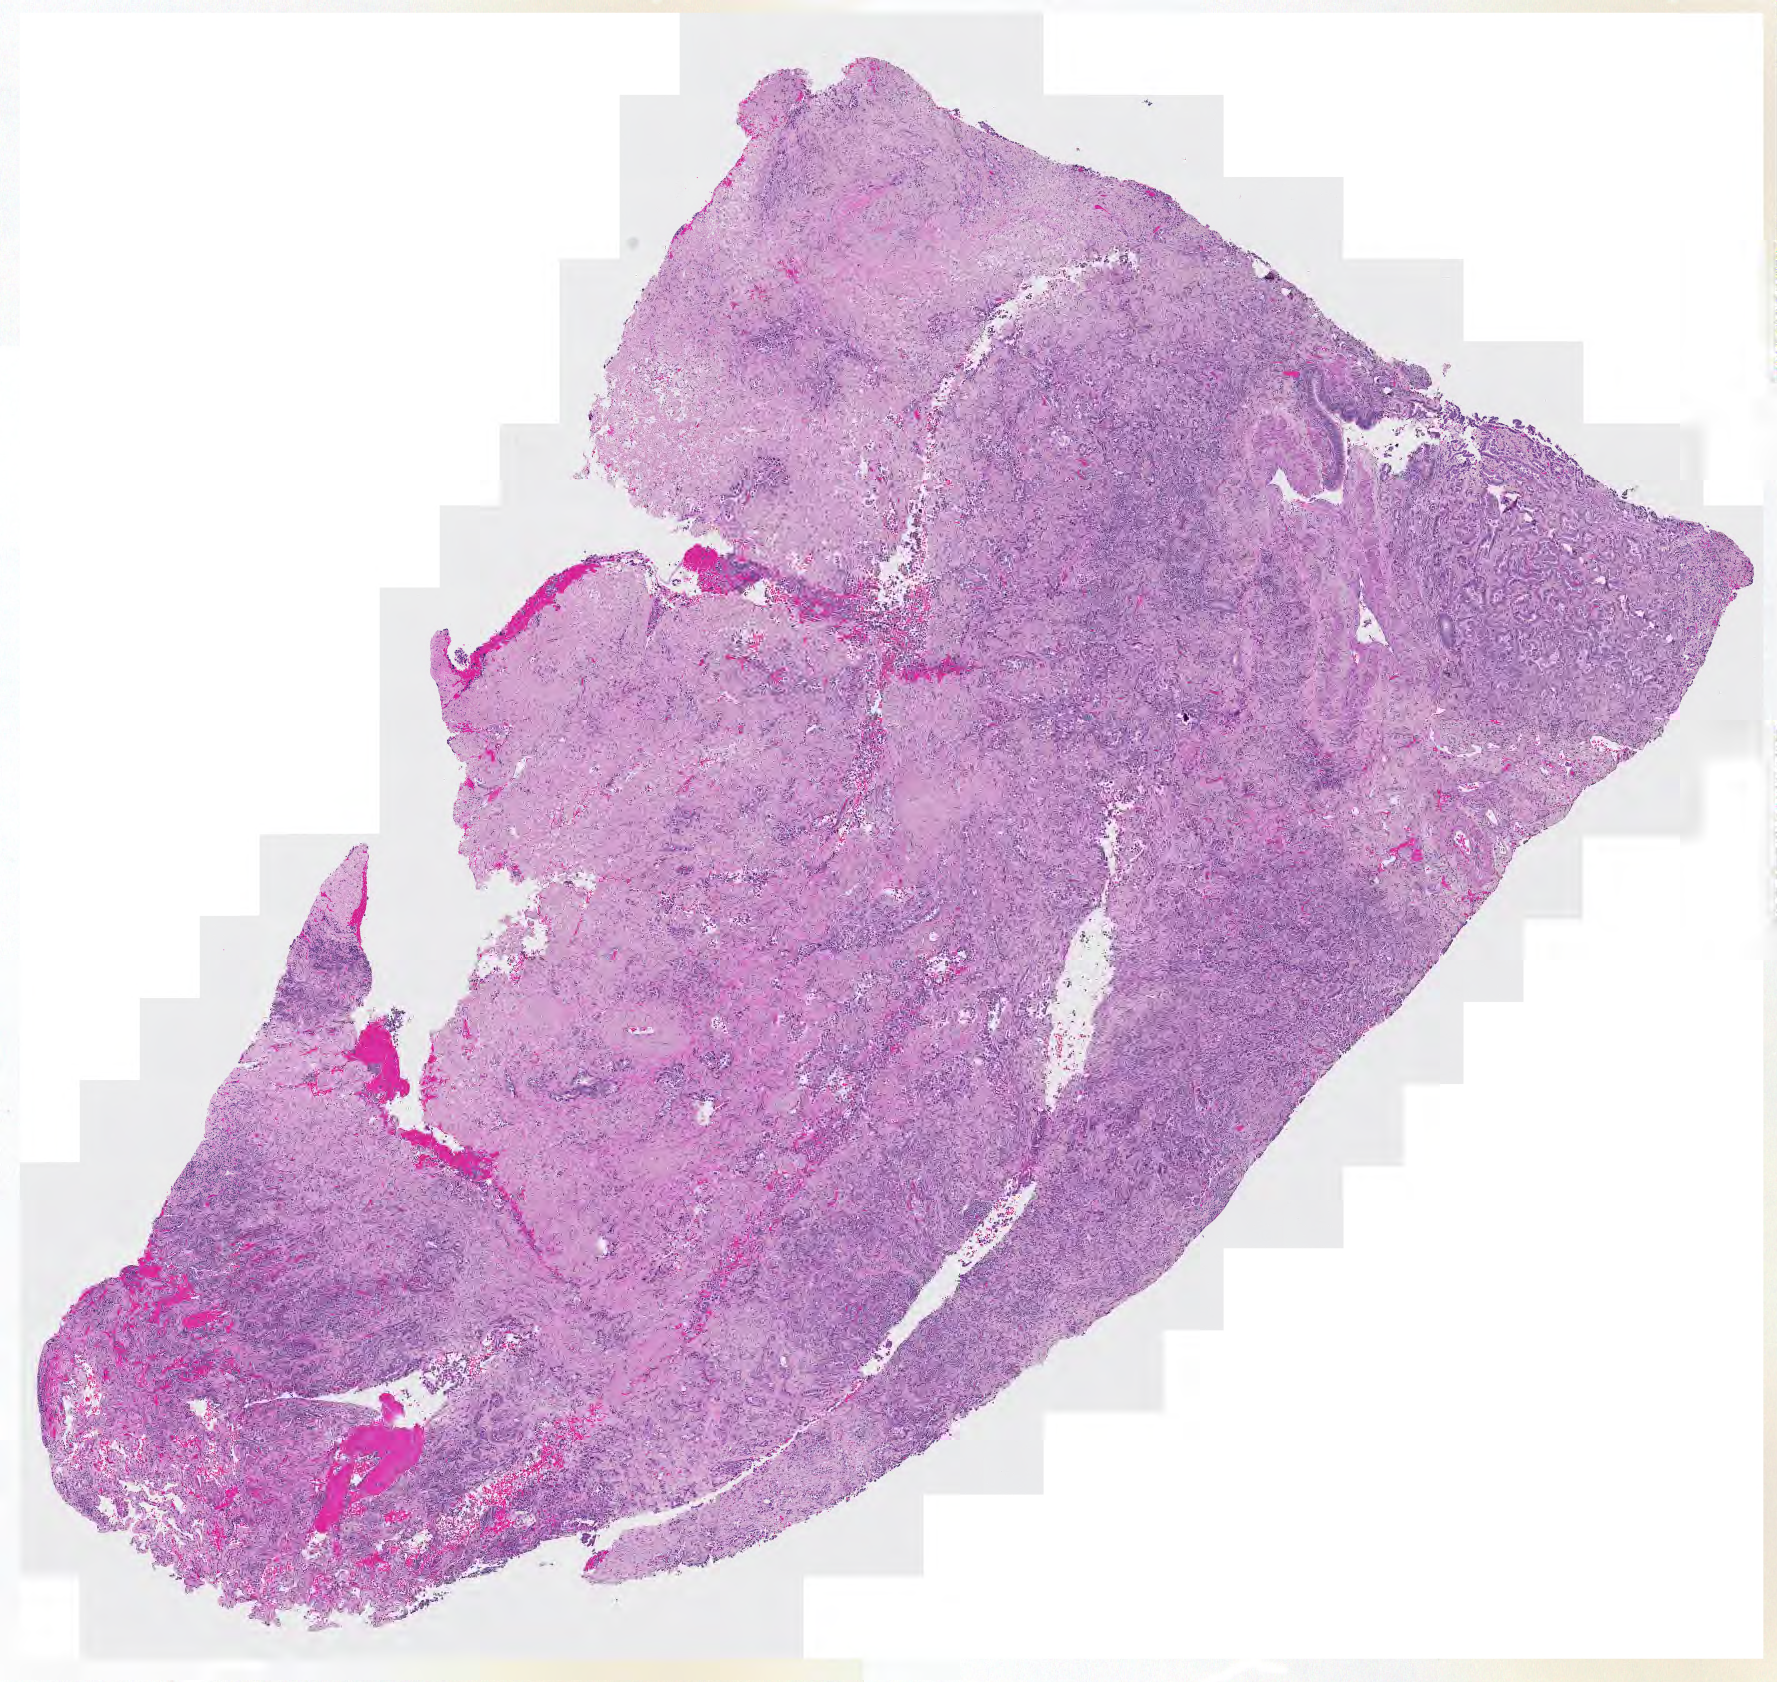
Whole-slide histology image, H&E-stained, shown as a low-resolution overview of the whole scanned area (about 9.2 x 8.7 mm, slide scanned at 20x); lung, tumour tissue. Female, 68 y/o. Histologic grade: G2 (moderately differentiated).
* primary tumour site (as recorded): right upper lobe
* diagnosis: Adenocarcinoma, NOS
* AJCC pathologic stage: IA